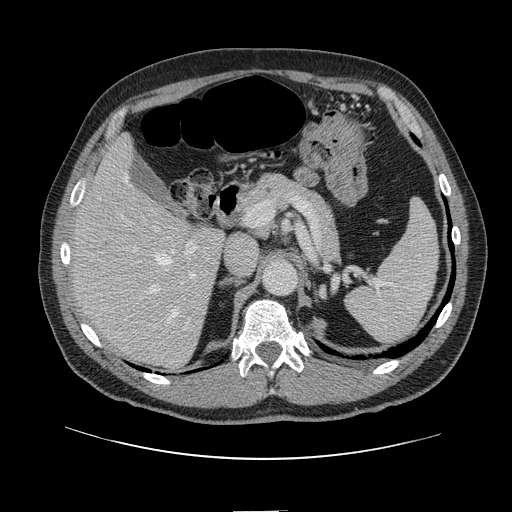
Contrast-enhanced abdominal CT, one axial slice. Intravenous contrast given. Soft-tissue window (W 400 / L 40 HU). 2.5 mm slice thickness. 512 × 512 image matrix, field of view 412 × 412 mm. Male patient, age 66 years. From the clinical record (not read from this slice): diagnosis: colorectal cancer liver metastases, imaged before liver resection; multiple liver metastases: no; largest metastasis: 3.5 cm; chemotherapy before resection: yes.
Outlined on this slice (expert manual segmentation):
- hepatic veins: bounding box (x1, y1, x2, y2) in pixels: (100, 174, 178, 323)
- liver: (75, 138, 223, 366)
- planned liver remnant (the part of the liver to remain after resection): (75, 138, 188, 300)
- portal vein (with intrahepatic branches): (118, 213, 198, 281)